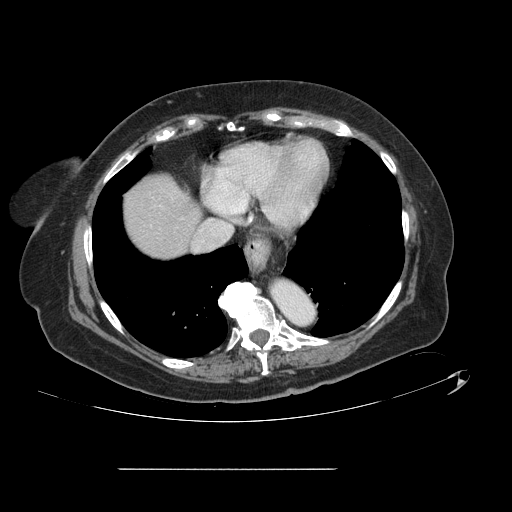
Contrast-enhanced abdominal CT, one axial slice; position 124 of 148 along the scan axis; intravenous contrast given; soft-tissue window (W 400 / L 40 HU); 512 × 512 image matrix. Female patient, age 75 years. Case-level facts recorded for this patient, not image findings: diagnosis: colorectal cancer liver metastases, imaged before liver resection; multiple liver metastases: no; largest metastasis: 2.4 cm; disease in both lobes: no.
Annotated regions visible in this slice (expert manual segmentation):
- liver: bounding box (x1, y1, x2, y2) in pixels: (125, 176, 200, 258)
- planned liver remnant (the part of the liver to remain after resection): (125, 176, 200, 258)